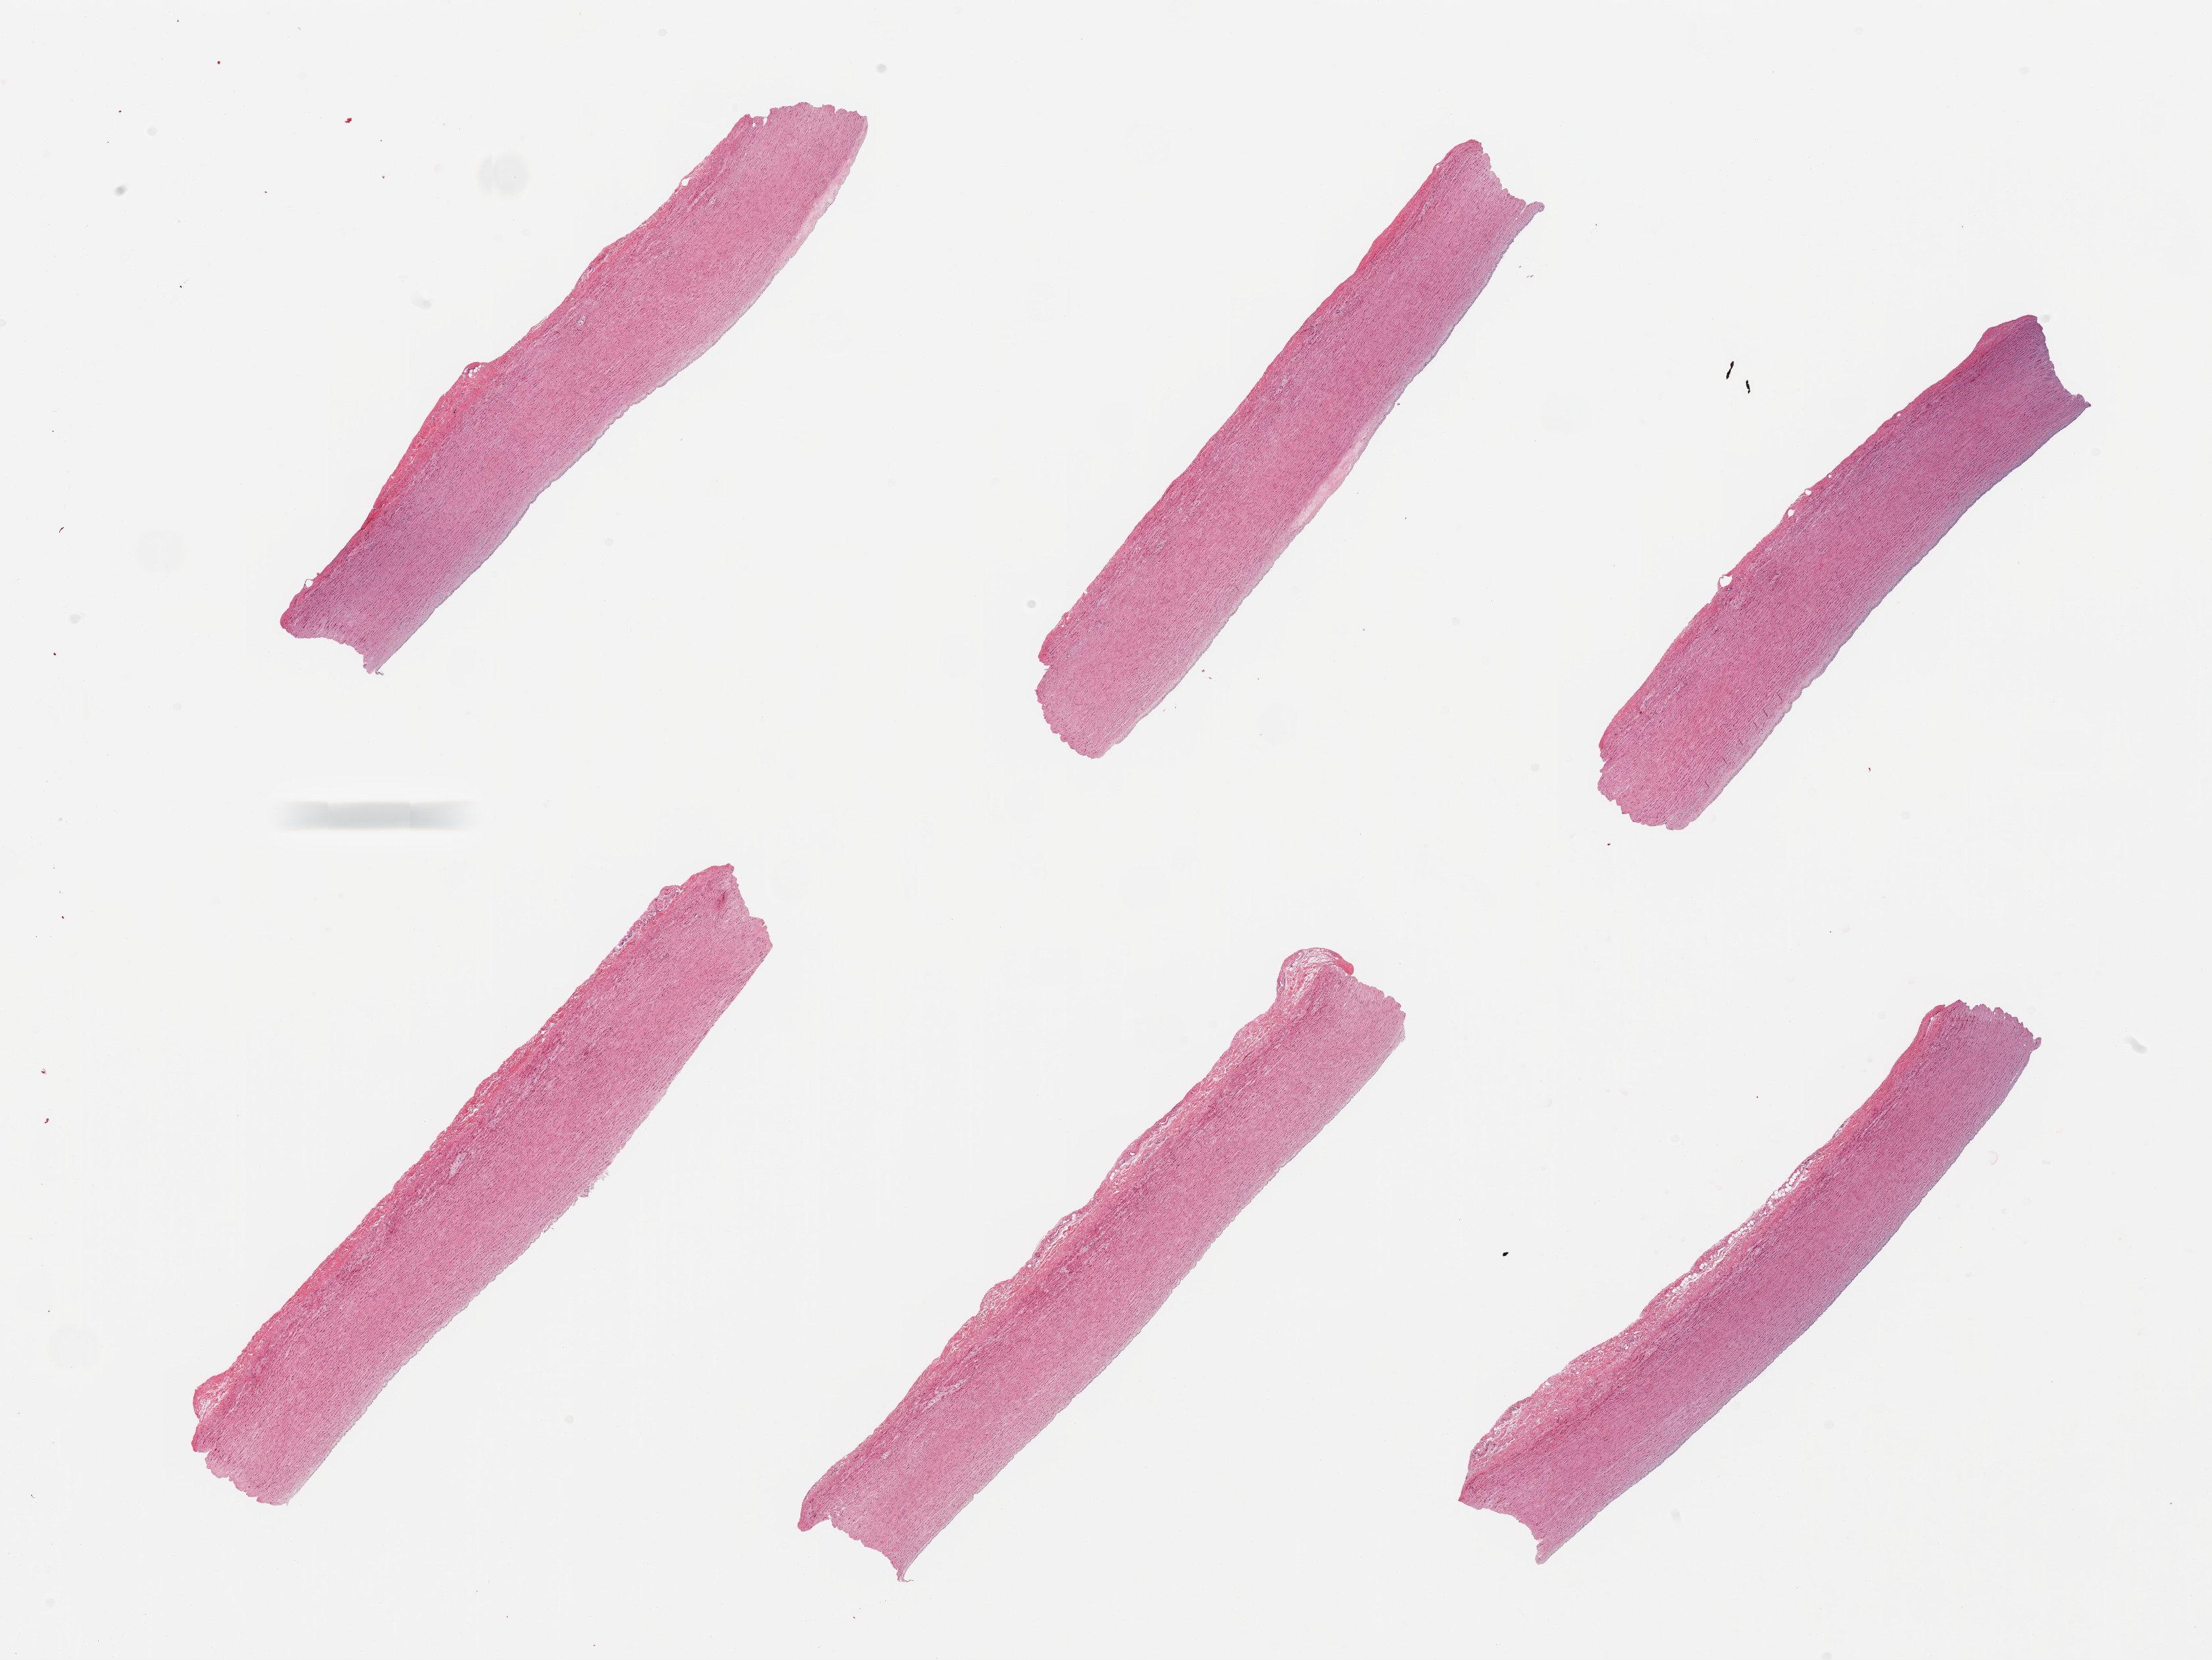
Digitized hematoxylin and eosin (H&E)-stained section, low-resolution overview of the scanned area, about 26.6 x 19.9 mm (from a 20x scan), PAXgene-fixed, paraffin-embedded tissue, section of aorta (target tissue), donor tissue sample. Female donor.
Reviewer comment on this tissue sample: 6 pieces, trace atherosis up to ~0.5mm.